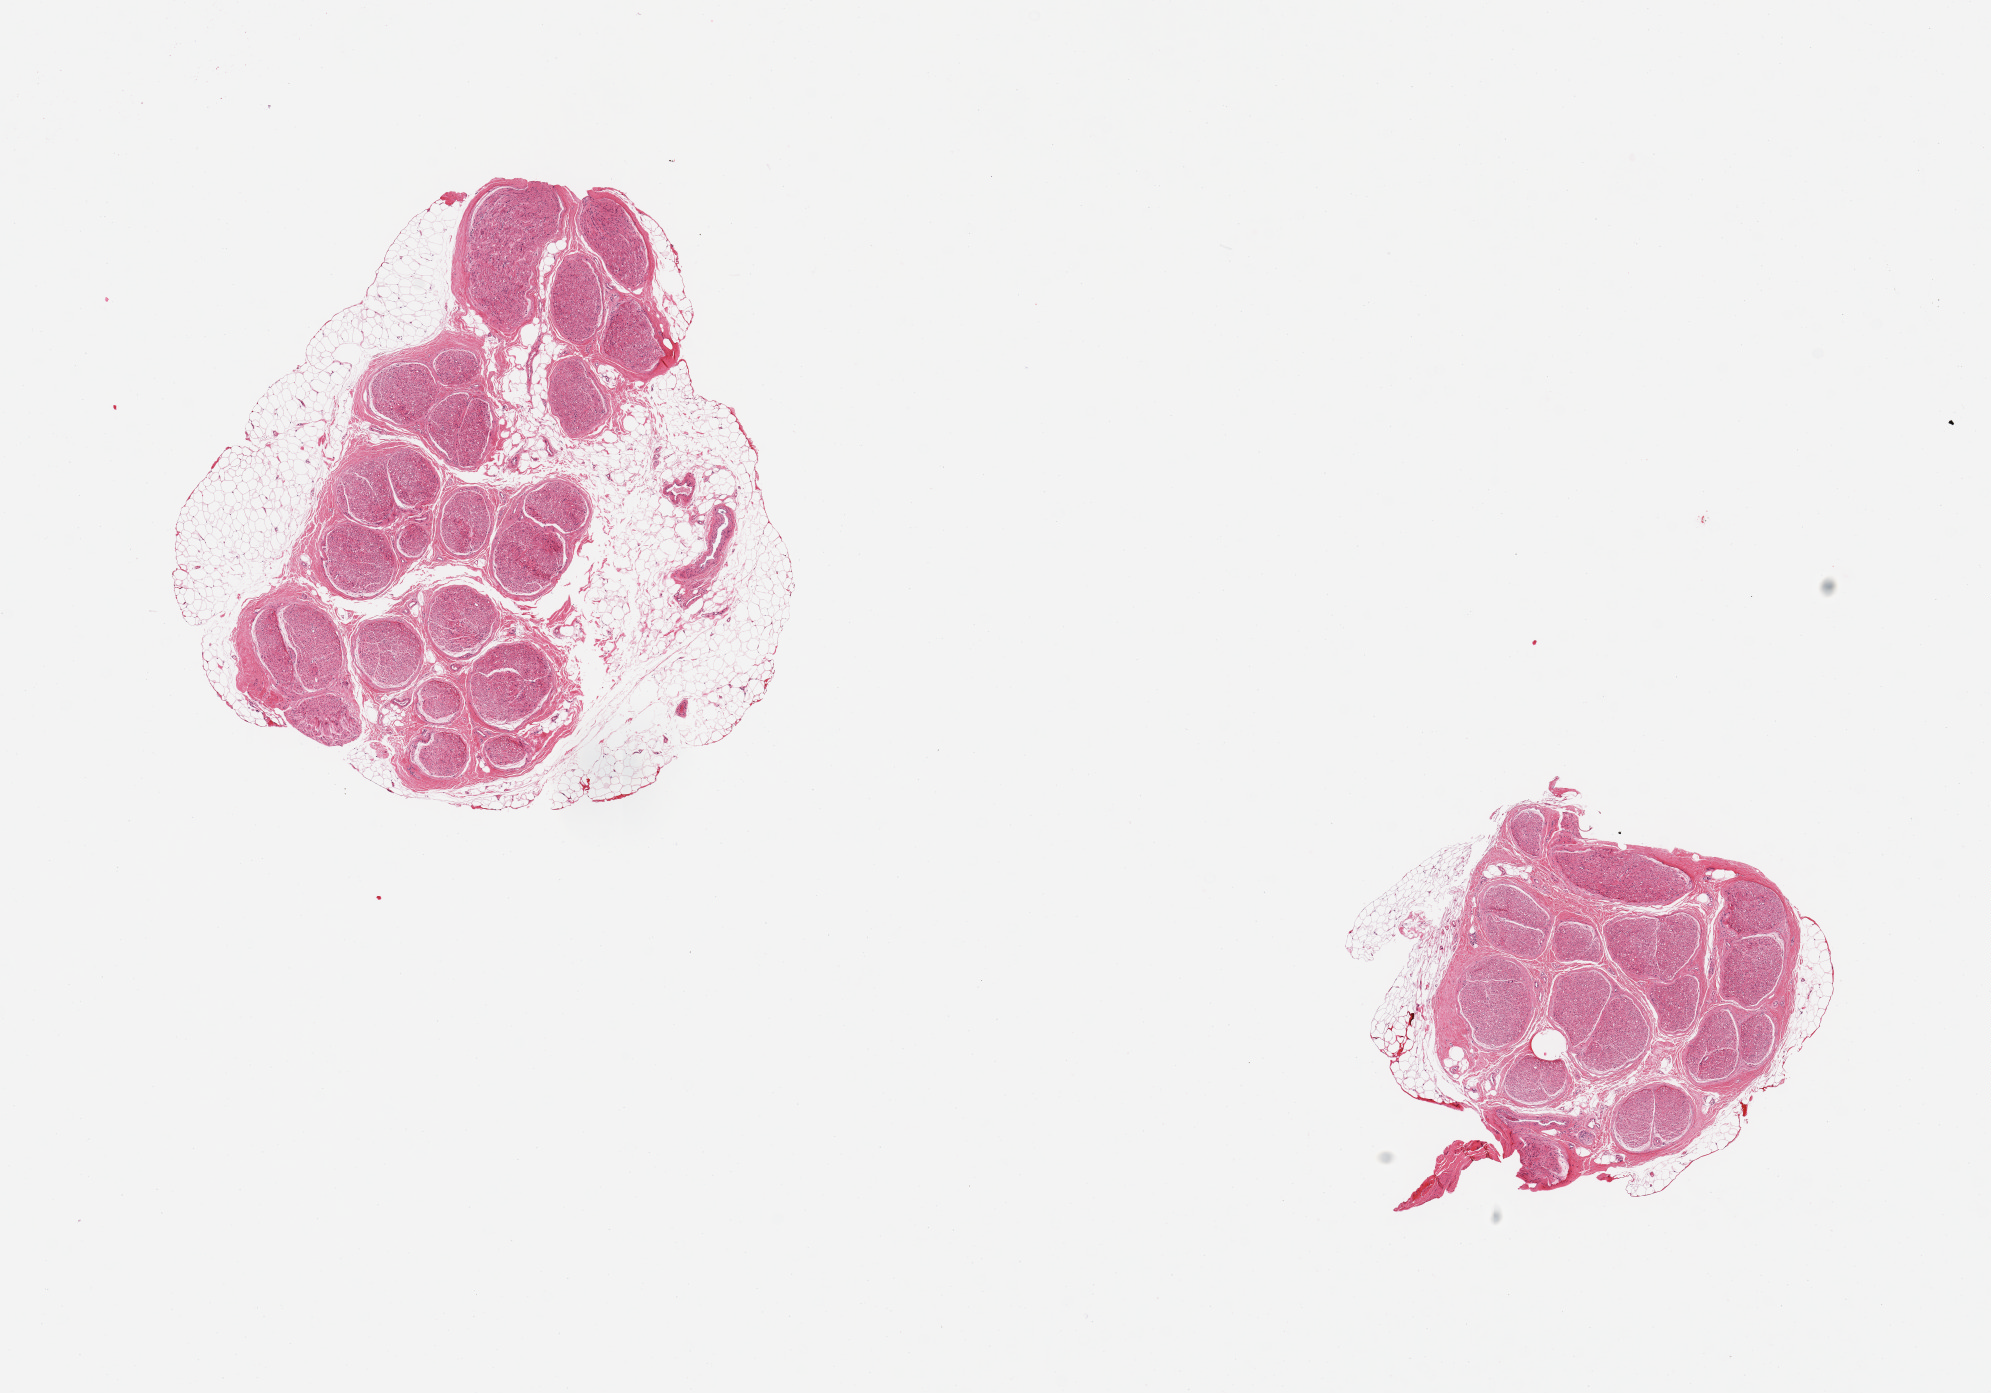
Whole-slide image, haematoxylin and eosin stain — whole scanned area (about 15.8 x 11.0 mm) shown as a low-resolution overview; PAXgene-fixed, paraffin-embedded tissue; section of tibial nerve (target tissue); donor tissue sample. Donor sex: female.
Review note (as recorded): 2 pieces: 1 with 50% external & internal fat, other with 10% external fat.